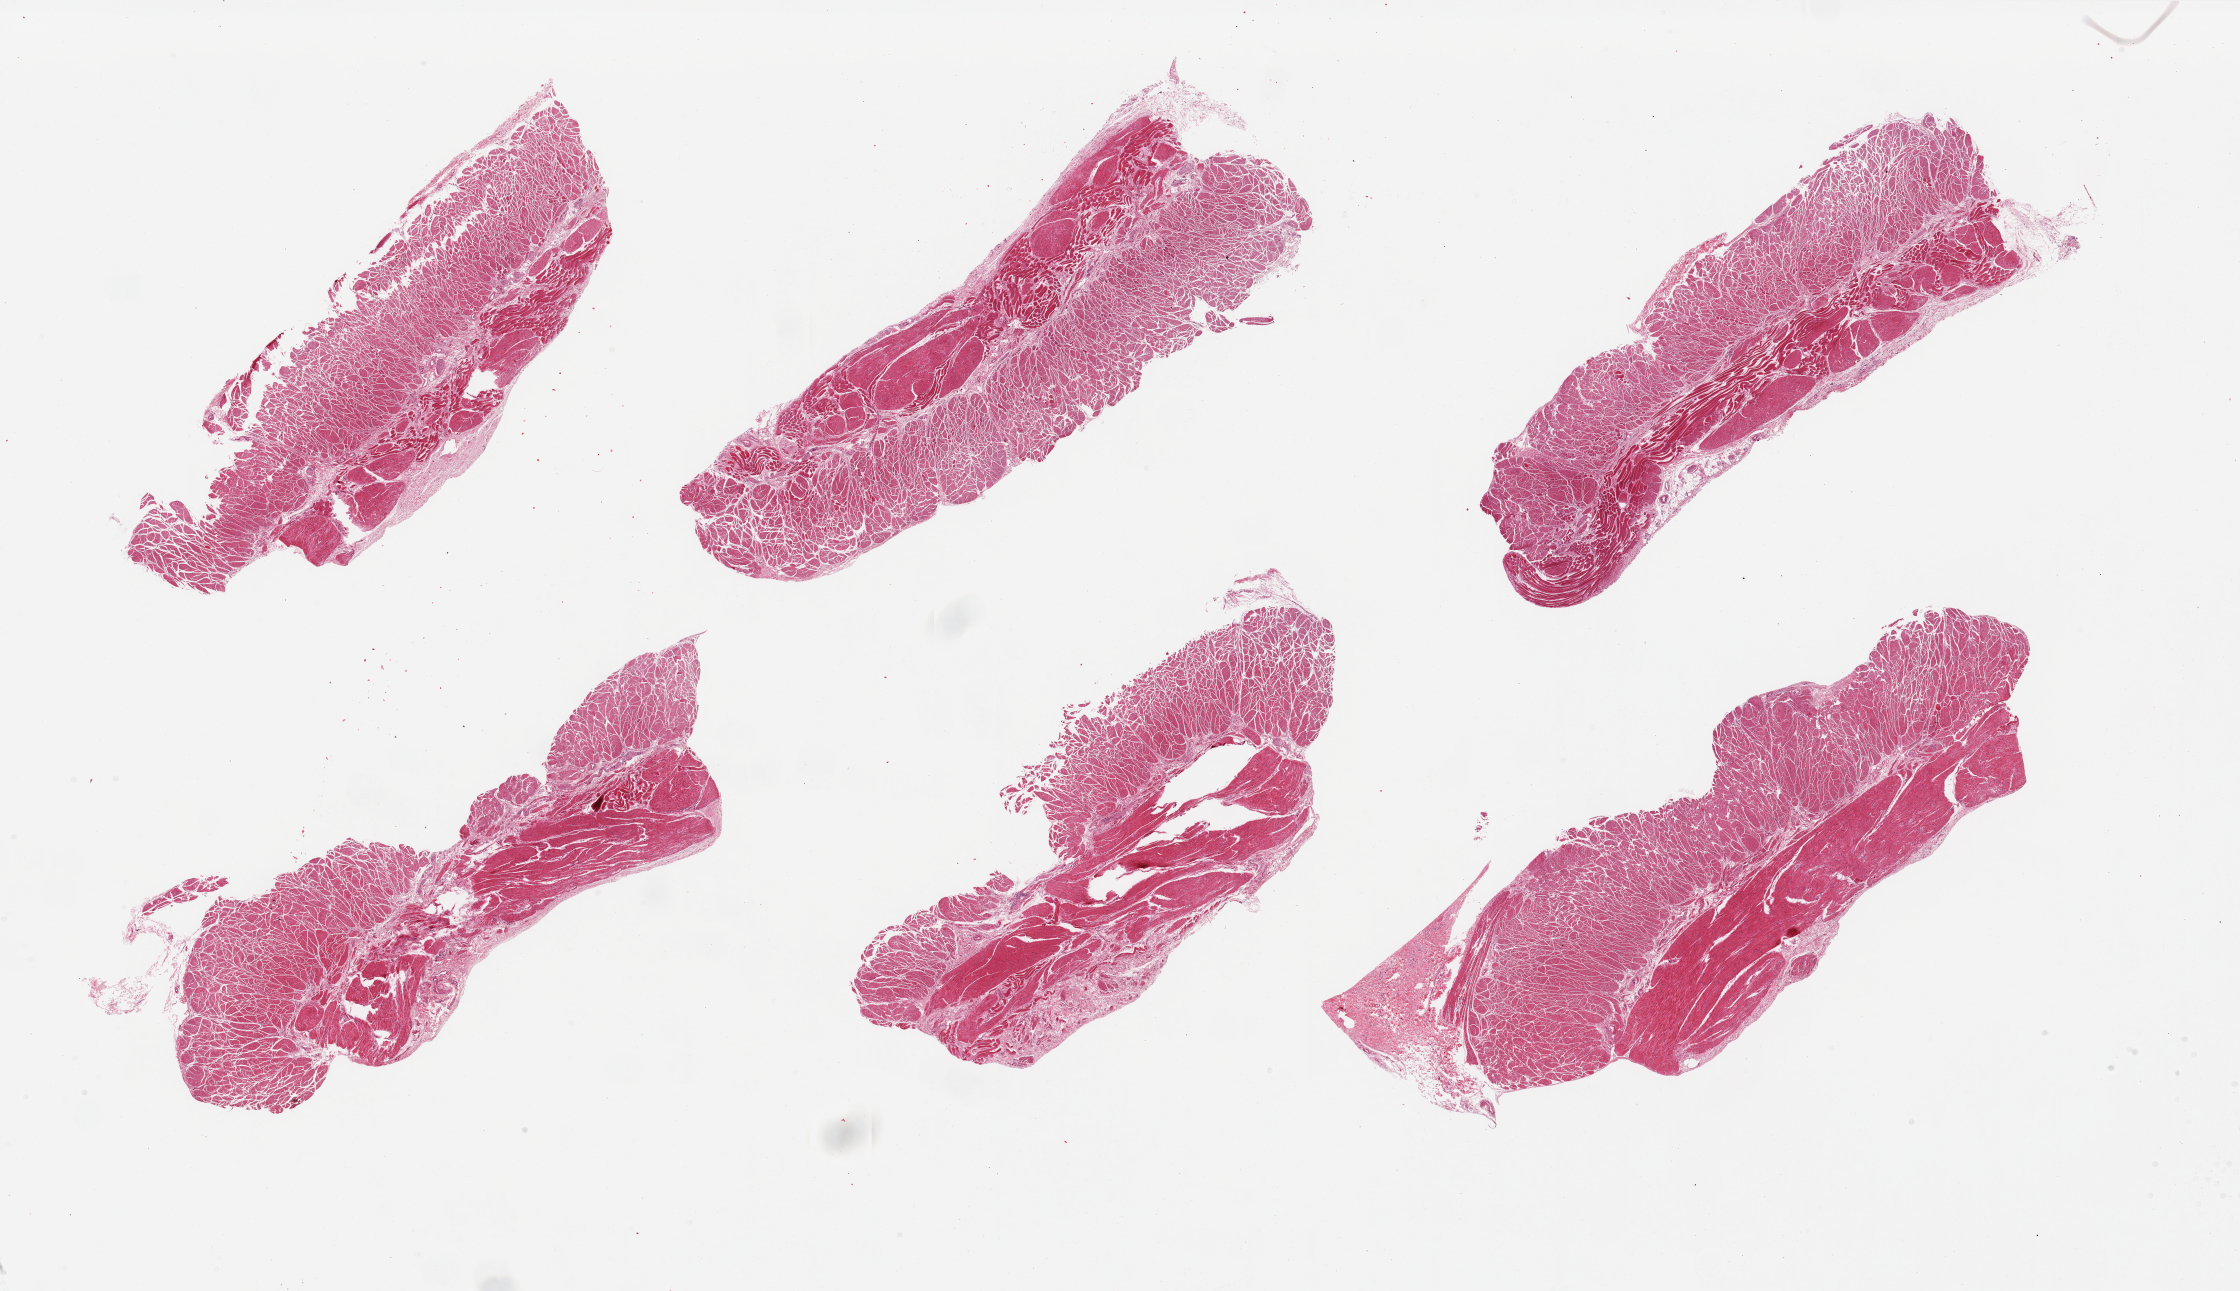
Digitized H&E-stained section — a low-resolution overview of the entire scanned area, about 35.4 x 20.4 mm. PAXgene-fixed paraffin-embedded (PFPE) section. Section of esophageal muscle (target tissue). Tissue donor sample. Donor sex: female.
Pathologist's review note for this sample: 6 pieces, all target muscularis, good specimens.